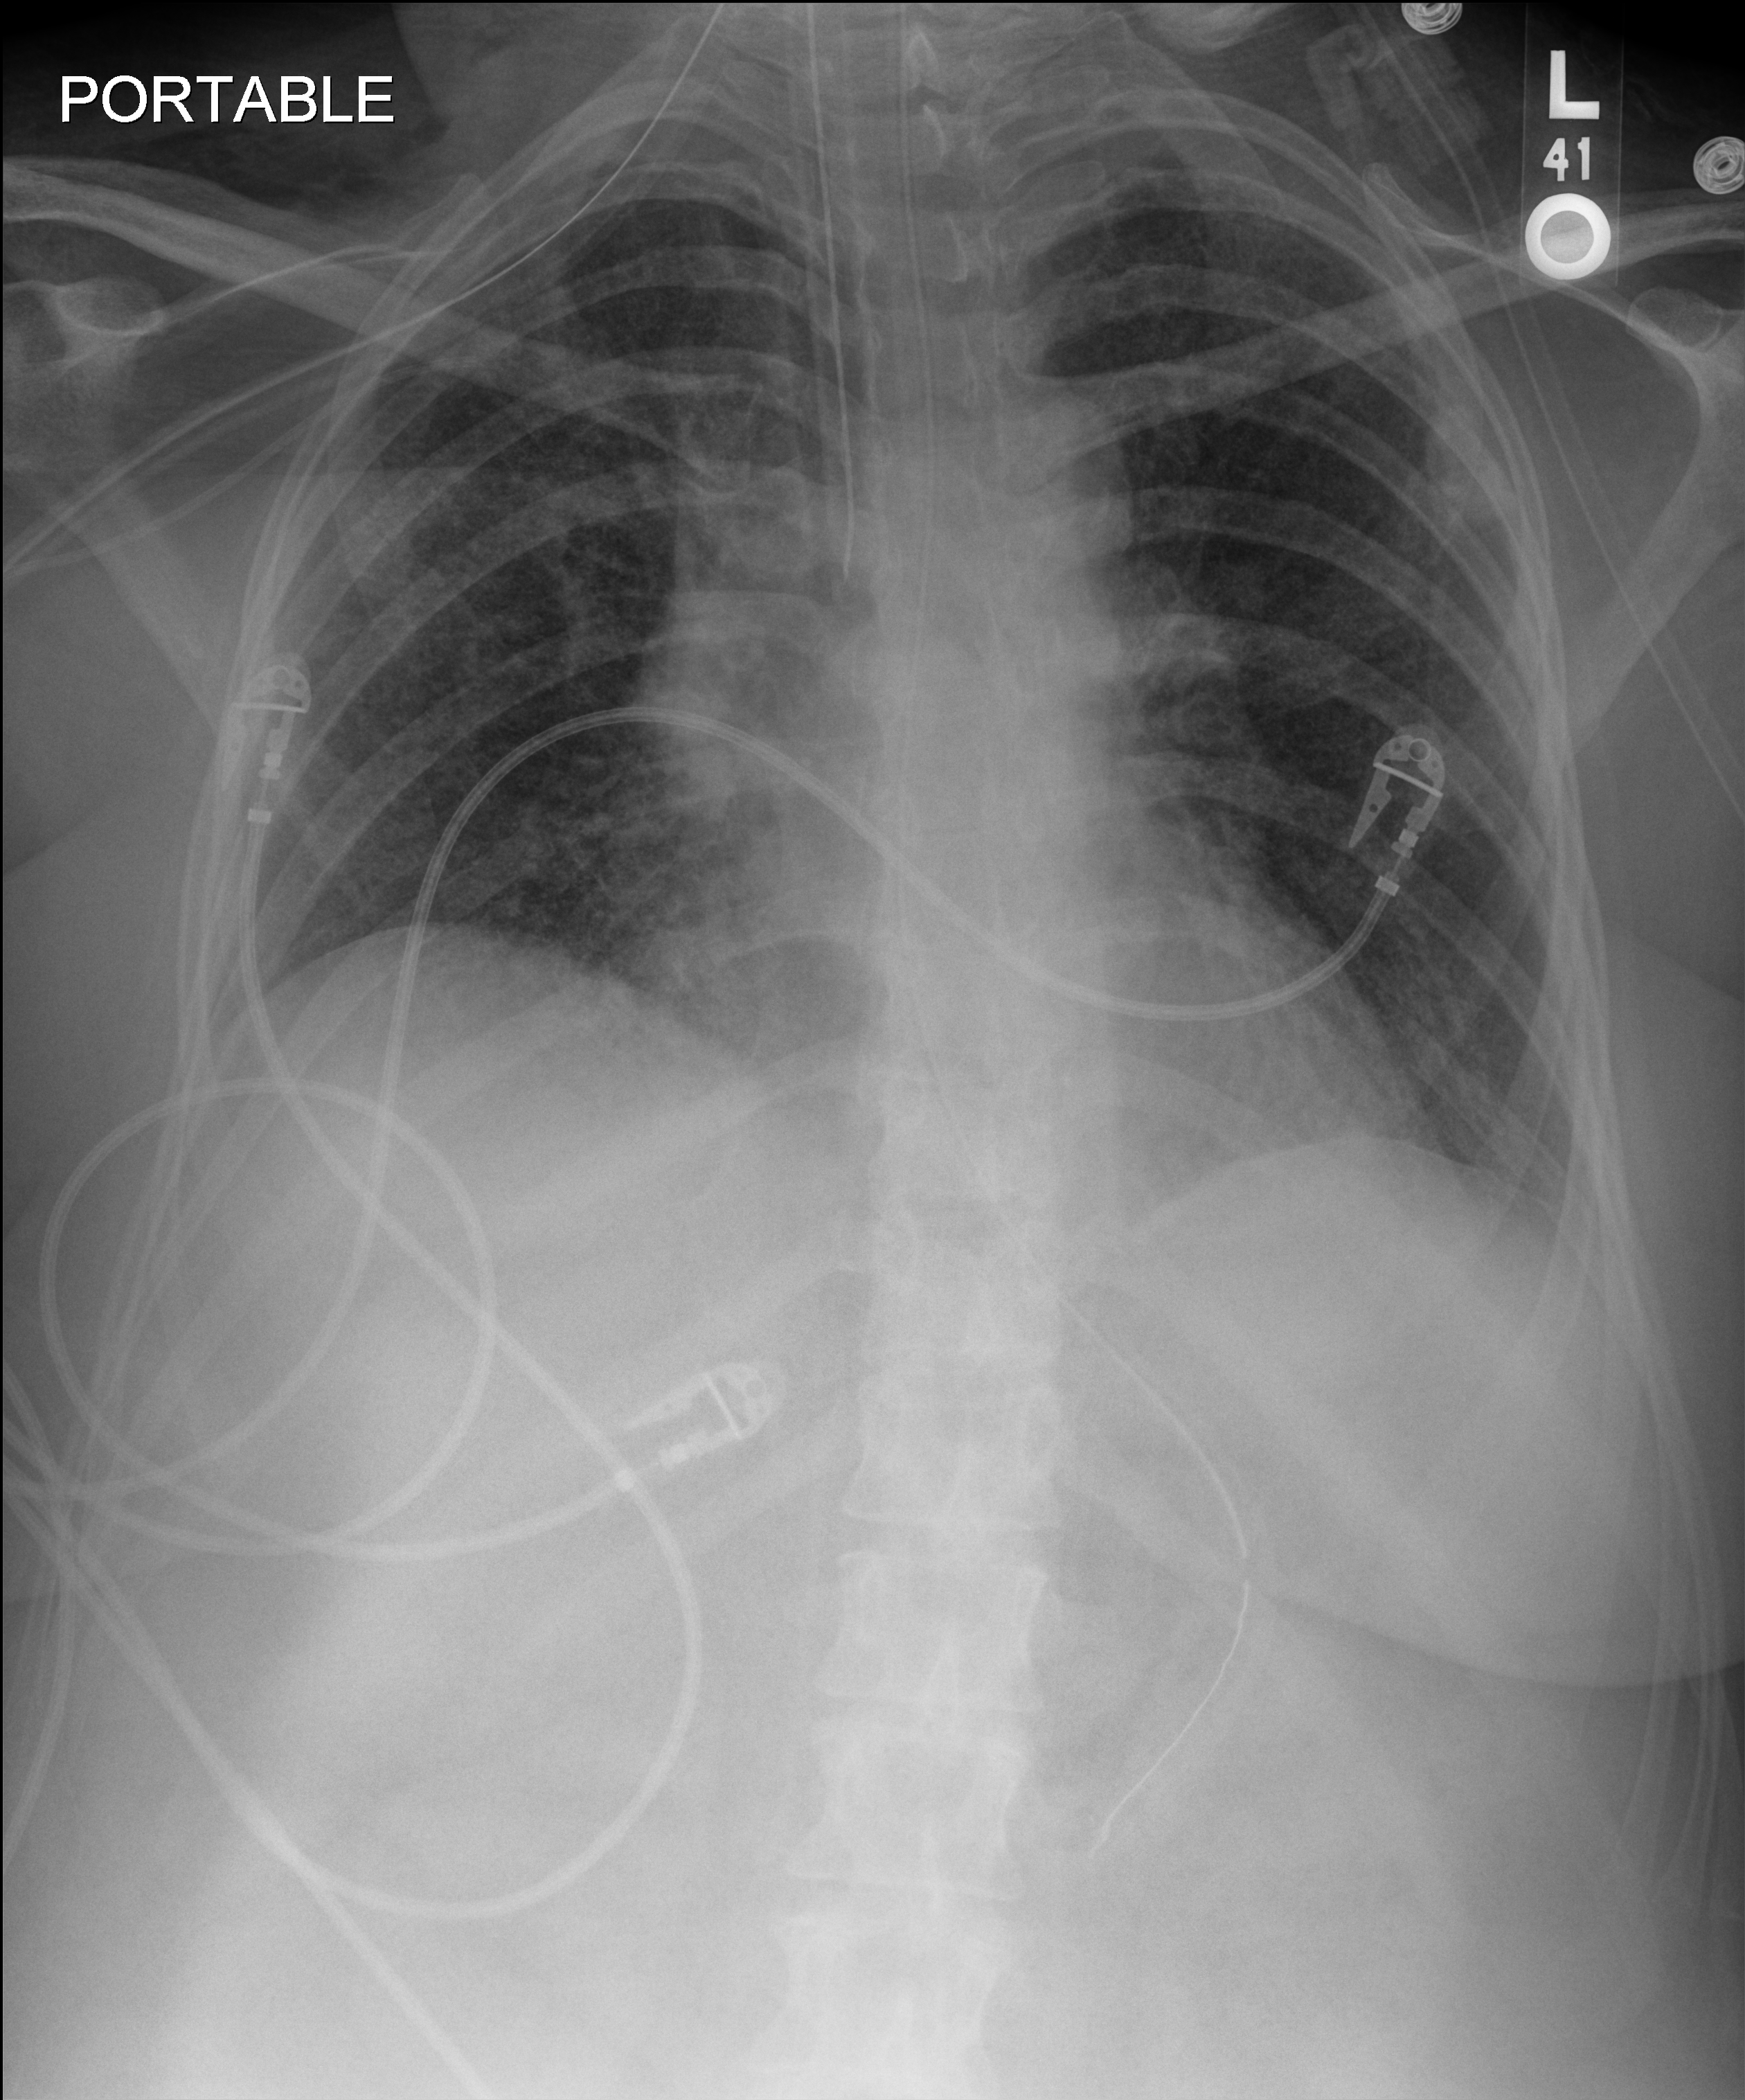
Chest radiograph (digital radiography); anteroposterior (AP) projection. Female patient hospitalised with COVID-19, age 18–59 years.
Hospital-stay facts (about this admission, not read from this image; timing relative to this image not recorded): mechanically ventilated during this hospital stay: yes.